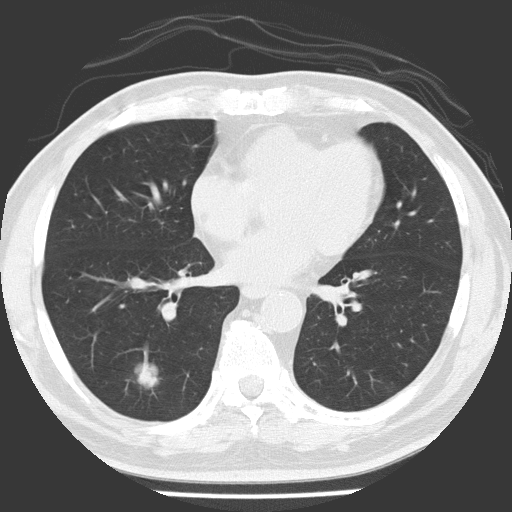
Low-dose screening chest CT, axial slice; first (baseline) screen; lung window (W 1500 / L -600 HU); 2 mm slice thickness; slice 87 of 154 in the series. Male participant, aged 56 years at enrolment.
- Expert-annotated lung lesion, box from (x=118, y=354) to (x=169, y=403) px.
- The exam's reader record, not a measurement of the box and not confirmed to be the same lesion: non-calcified nodule or mass ≥4 mm, right lower lobe, 21 × 17 mm, spiculated (stellate) margins, soft tissue attenuation.
- Official screen result: positive, change unspecified: nodule(s) >= 4 mm or enlarging nodule(s), mass(es), or other non-specific abnormalities suspicious for lung cancer.
- Later outcome: lung cancer diagnosed 84 days after this screen — adenocarcinoma, NOS, right lower lobe, poorly differentiated (G3), stage IA (AJCC 6th edition), 24 mm at pathology.